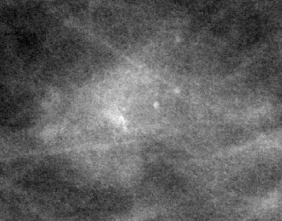
Cropped region of a digitized screen-film mammogram centred on a radiologist-marked abnormality; right breast; CC view.
Mass, shape lobulated, margins circumscribed / ill defined; BI-RADS assessment category 4; subtlety rating 3 on a 1 (subtle) to 5 (obvious) scale; pathology (as recorded): benign.